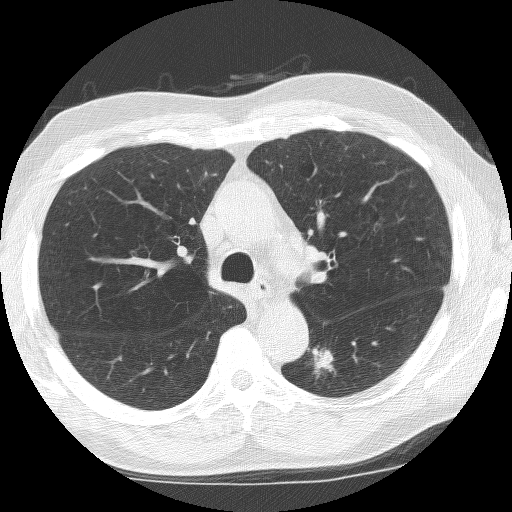
Axial slice from a low-dose chest CT screening exam. First (baseline) screen. Lung window (W 1500 / L -600 HU). 120 kVp. 512 × 512 image matrix. Male participant, aged 67 years at enrolment.
Expert reader's lesion annotation, bounding box [x1, y1, x2, y2] px = [295, 340, 342, 388]. Reader record for this screening exam (exam-level; its link to the box is not recorded): non-calcified nodule or mass ≥4 mm, left lower lobe, 18 × 13 mm, spiculated (stellate) margins, soft tissue attenuation. Lung cancer was diagnosed 5 days after this screen: non-small cell carcinoma, left lower lobe, undifferentiated (G4), stage IA (AJCC 6th edition), 12 mm at pathology.